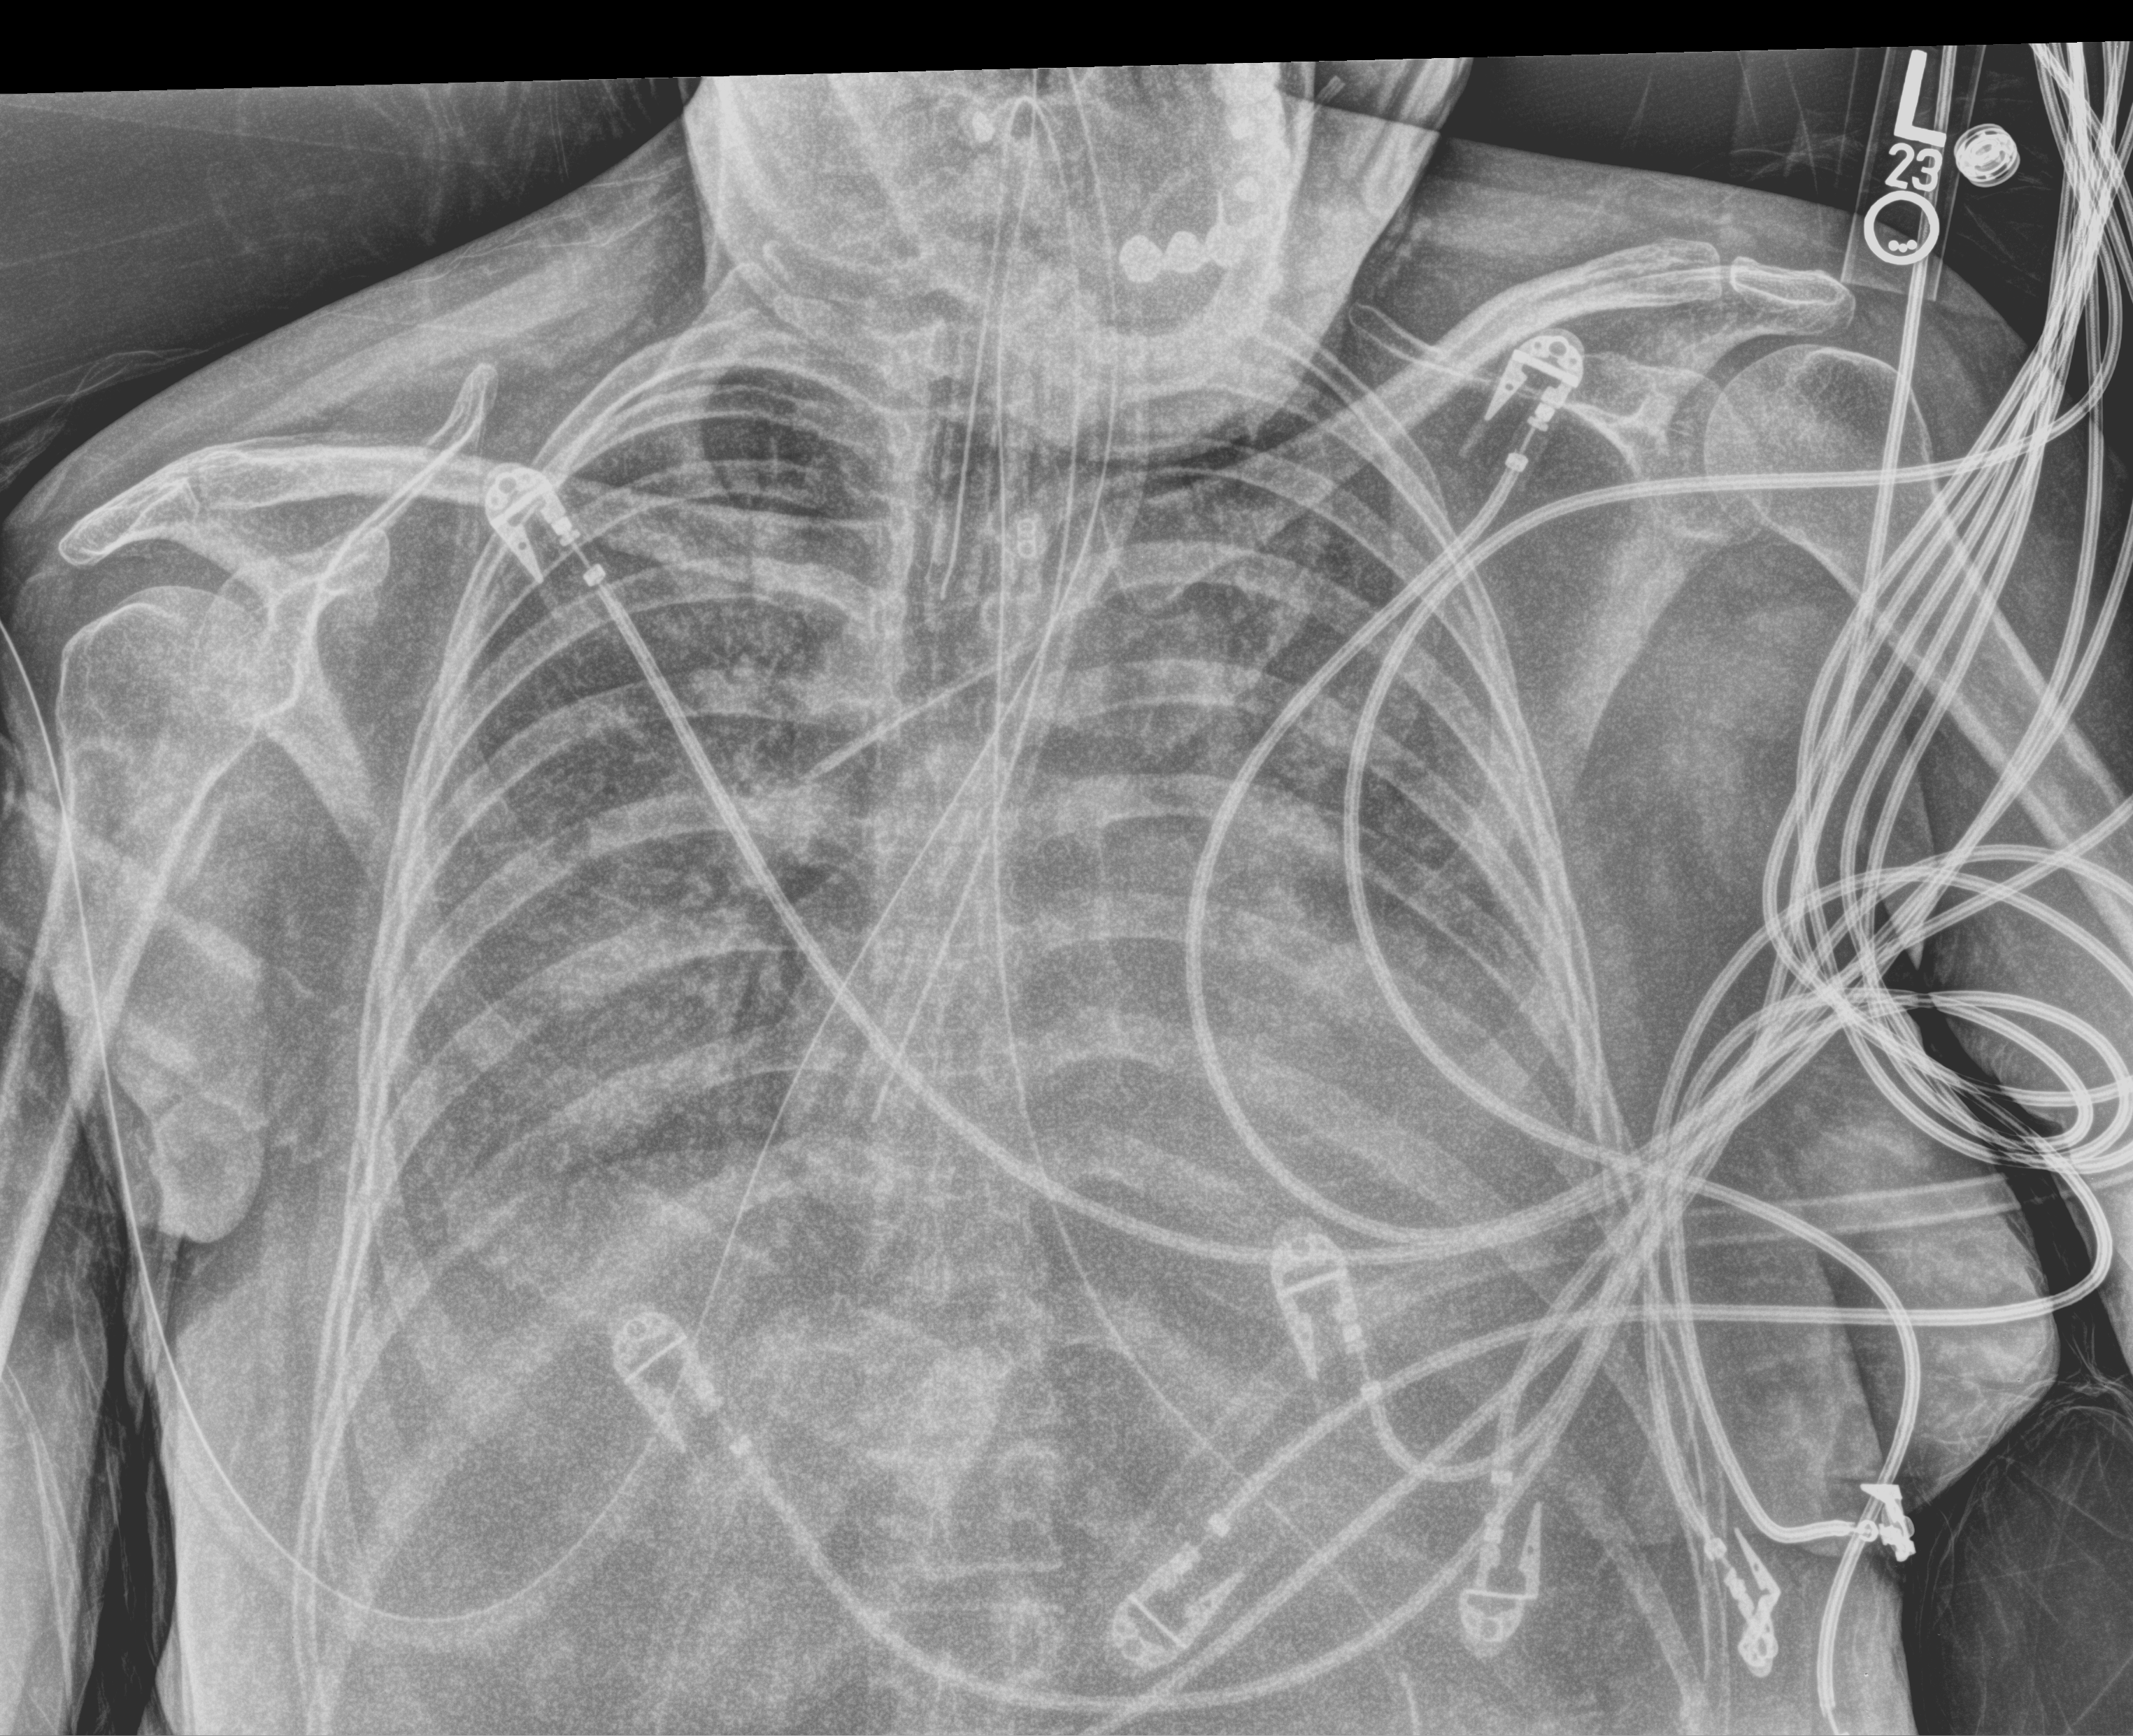
Bedside chest radiograph (computed radiography); anteroposterior (AP) projection. Adult patient hospitalised with COVID-19, age 18–59 years.
Admission-level facts for this patient (not findings on this image; timing relative to this image not recorded): admitted to intensive care during this hospital stay: yes; mechanically ventilated during this hospital stay: yes; length of hospital stay: 10 days.